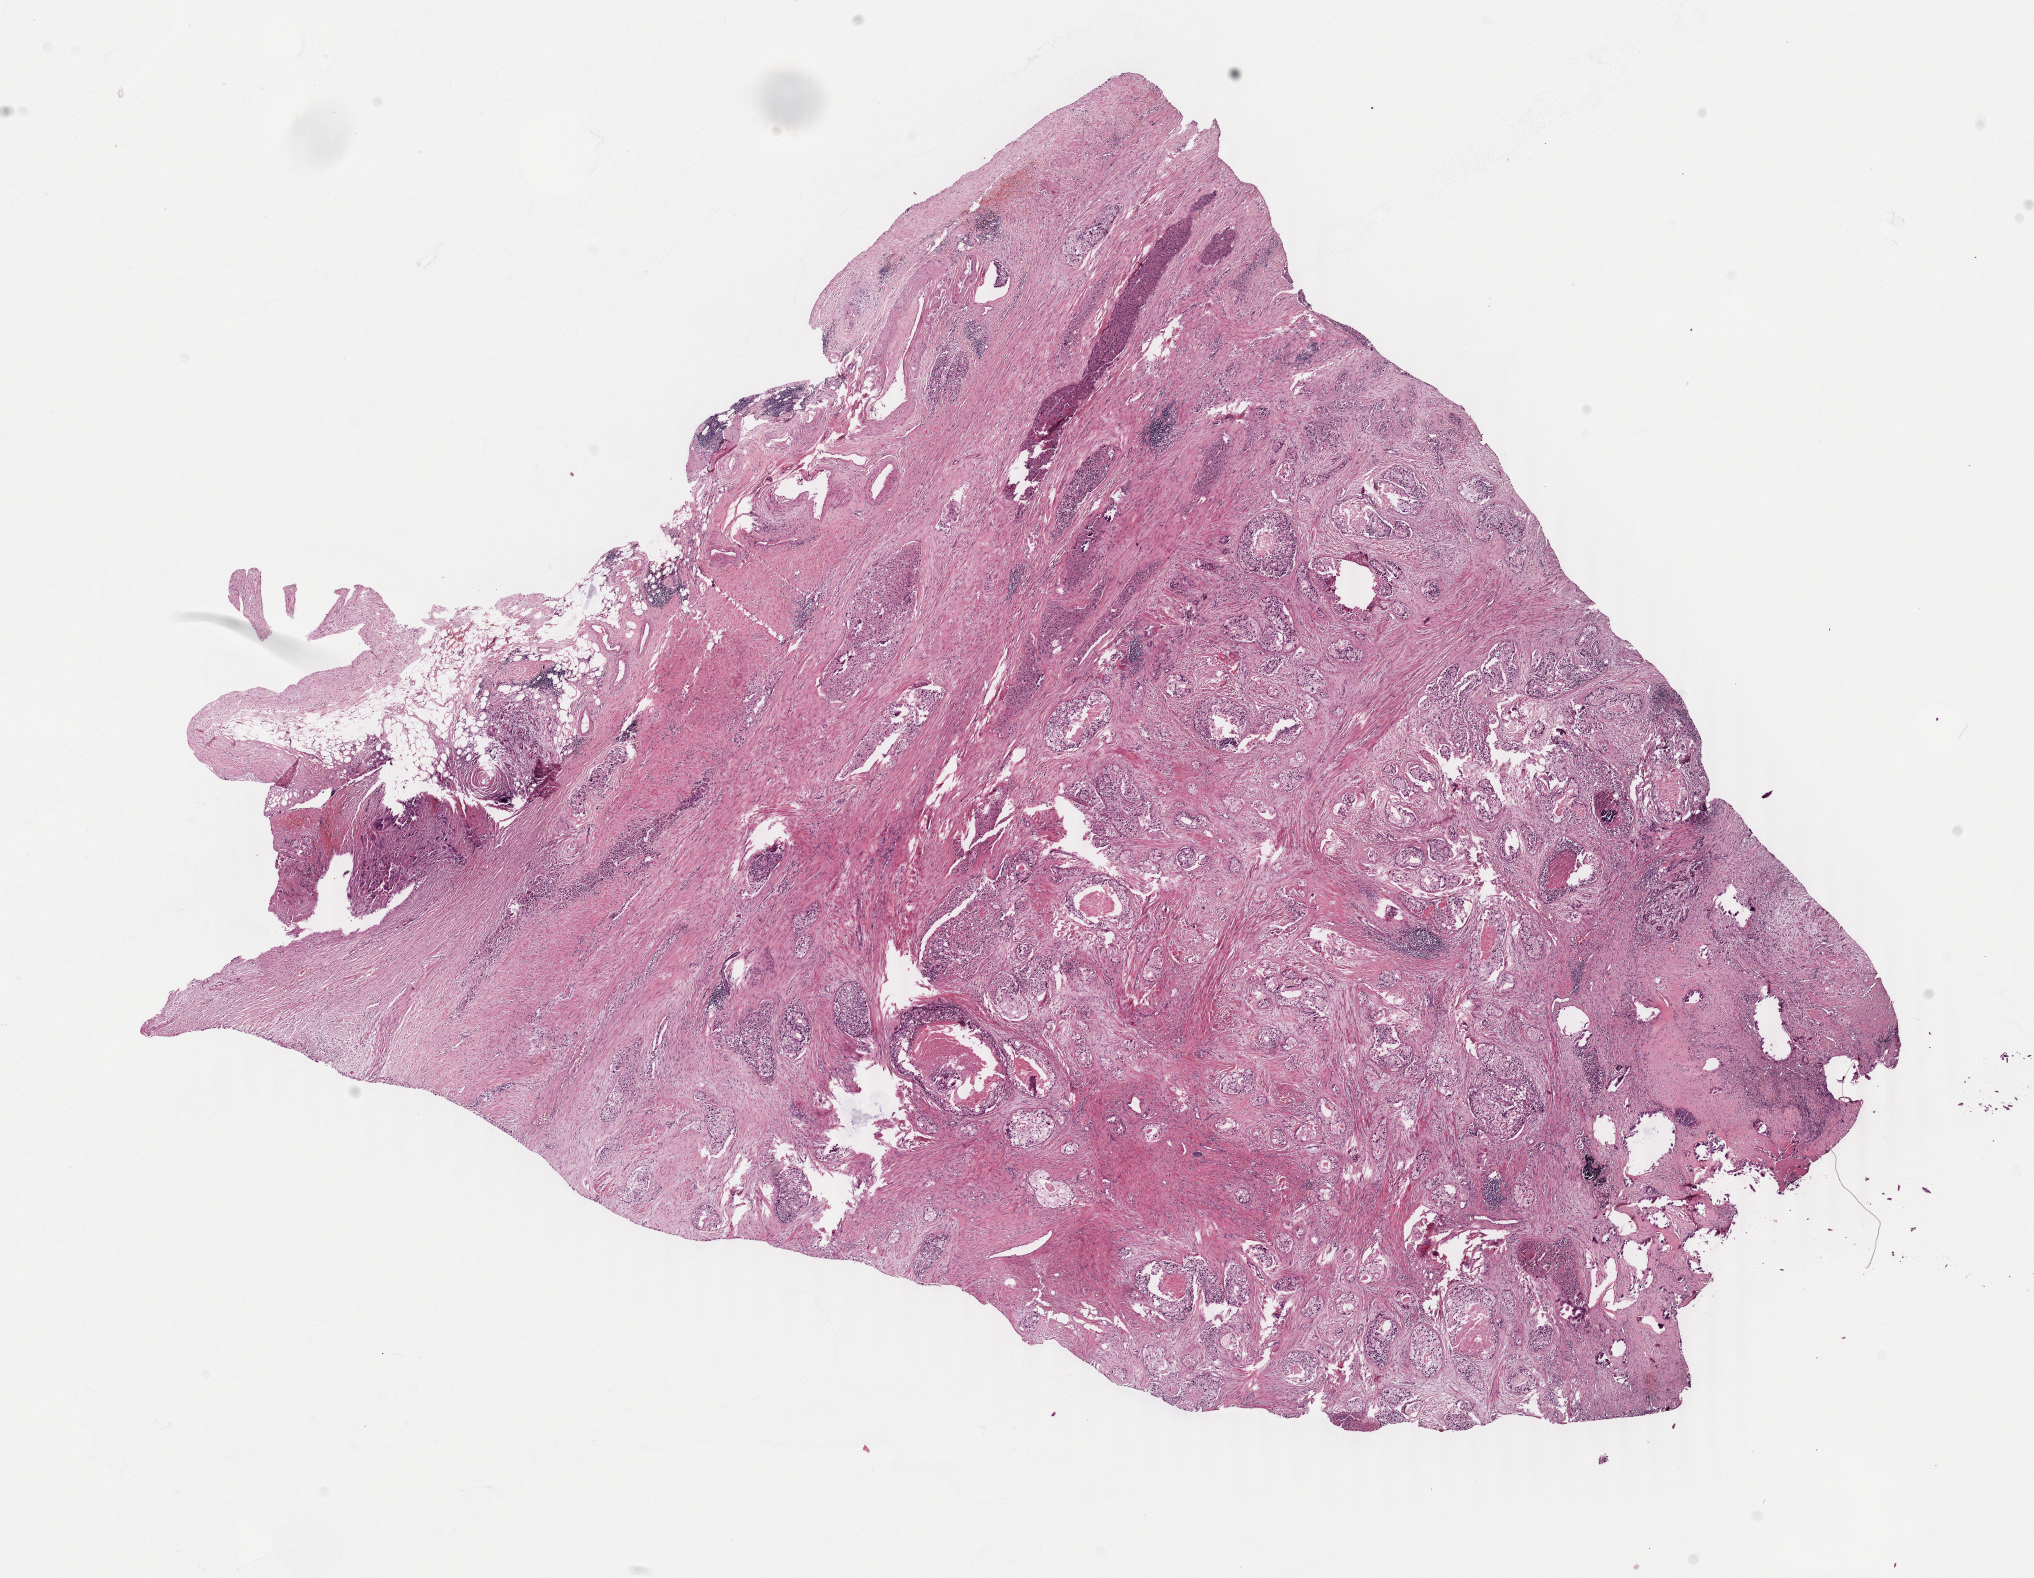
Hematoxylin and eosin (H&E) stained whole-slide image — a low-resolution overview of the entire scanned area, about 16.2 x 12.6 mm (slide scanned at 40x); formalin-fixed paraffin-embedded (FFPE) diagnostic section; primary tumour sample from the prostate. Male, age 64 years at initial diagnosis. Gleason score: 8 (4+4).
Histologic diagnosis: Adenocarcinoma, NOS (prostate gland).